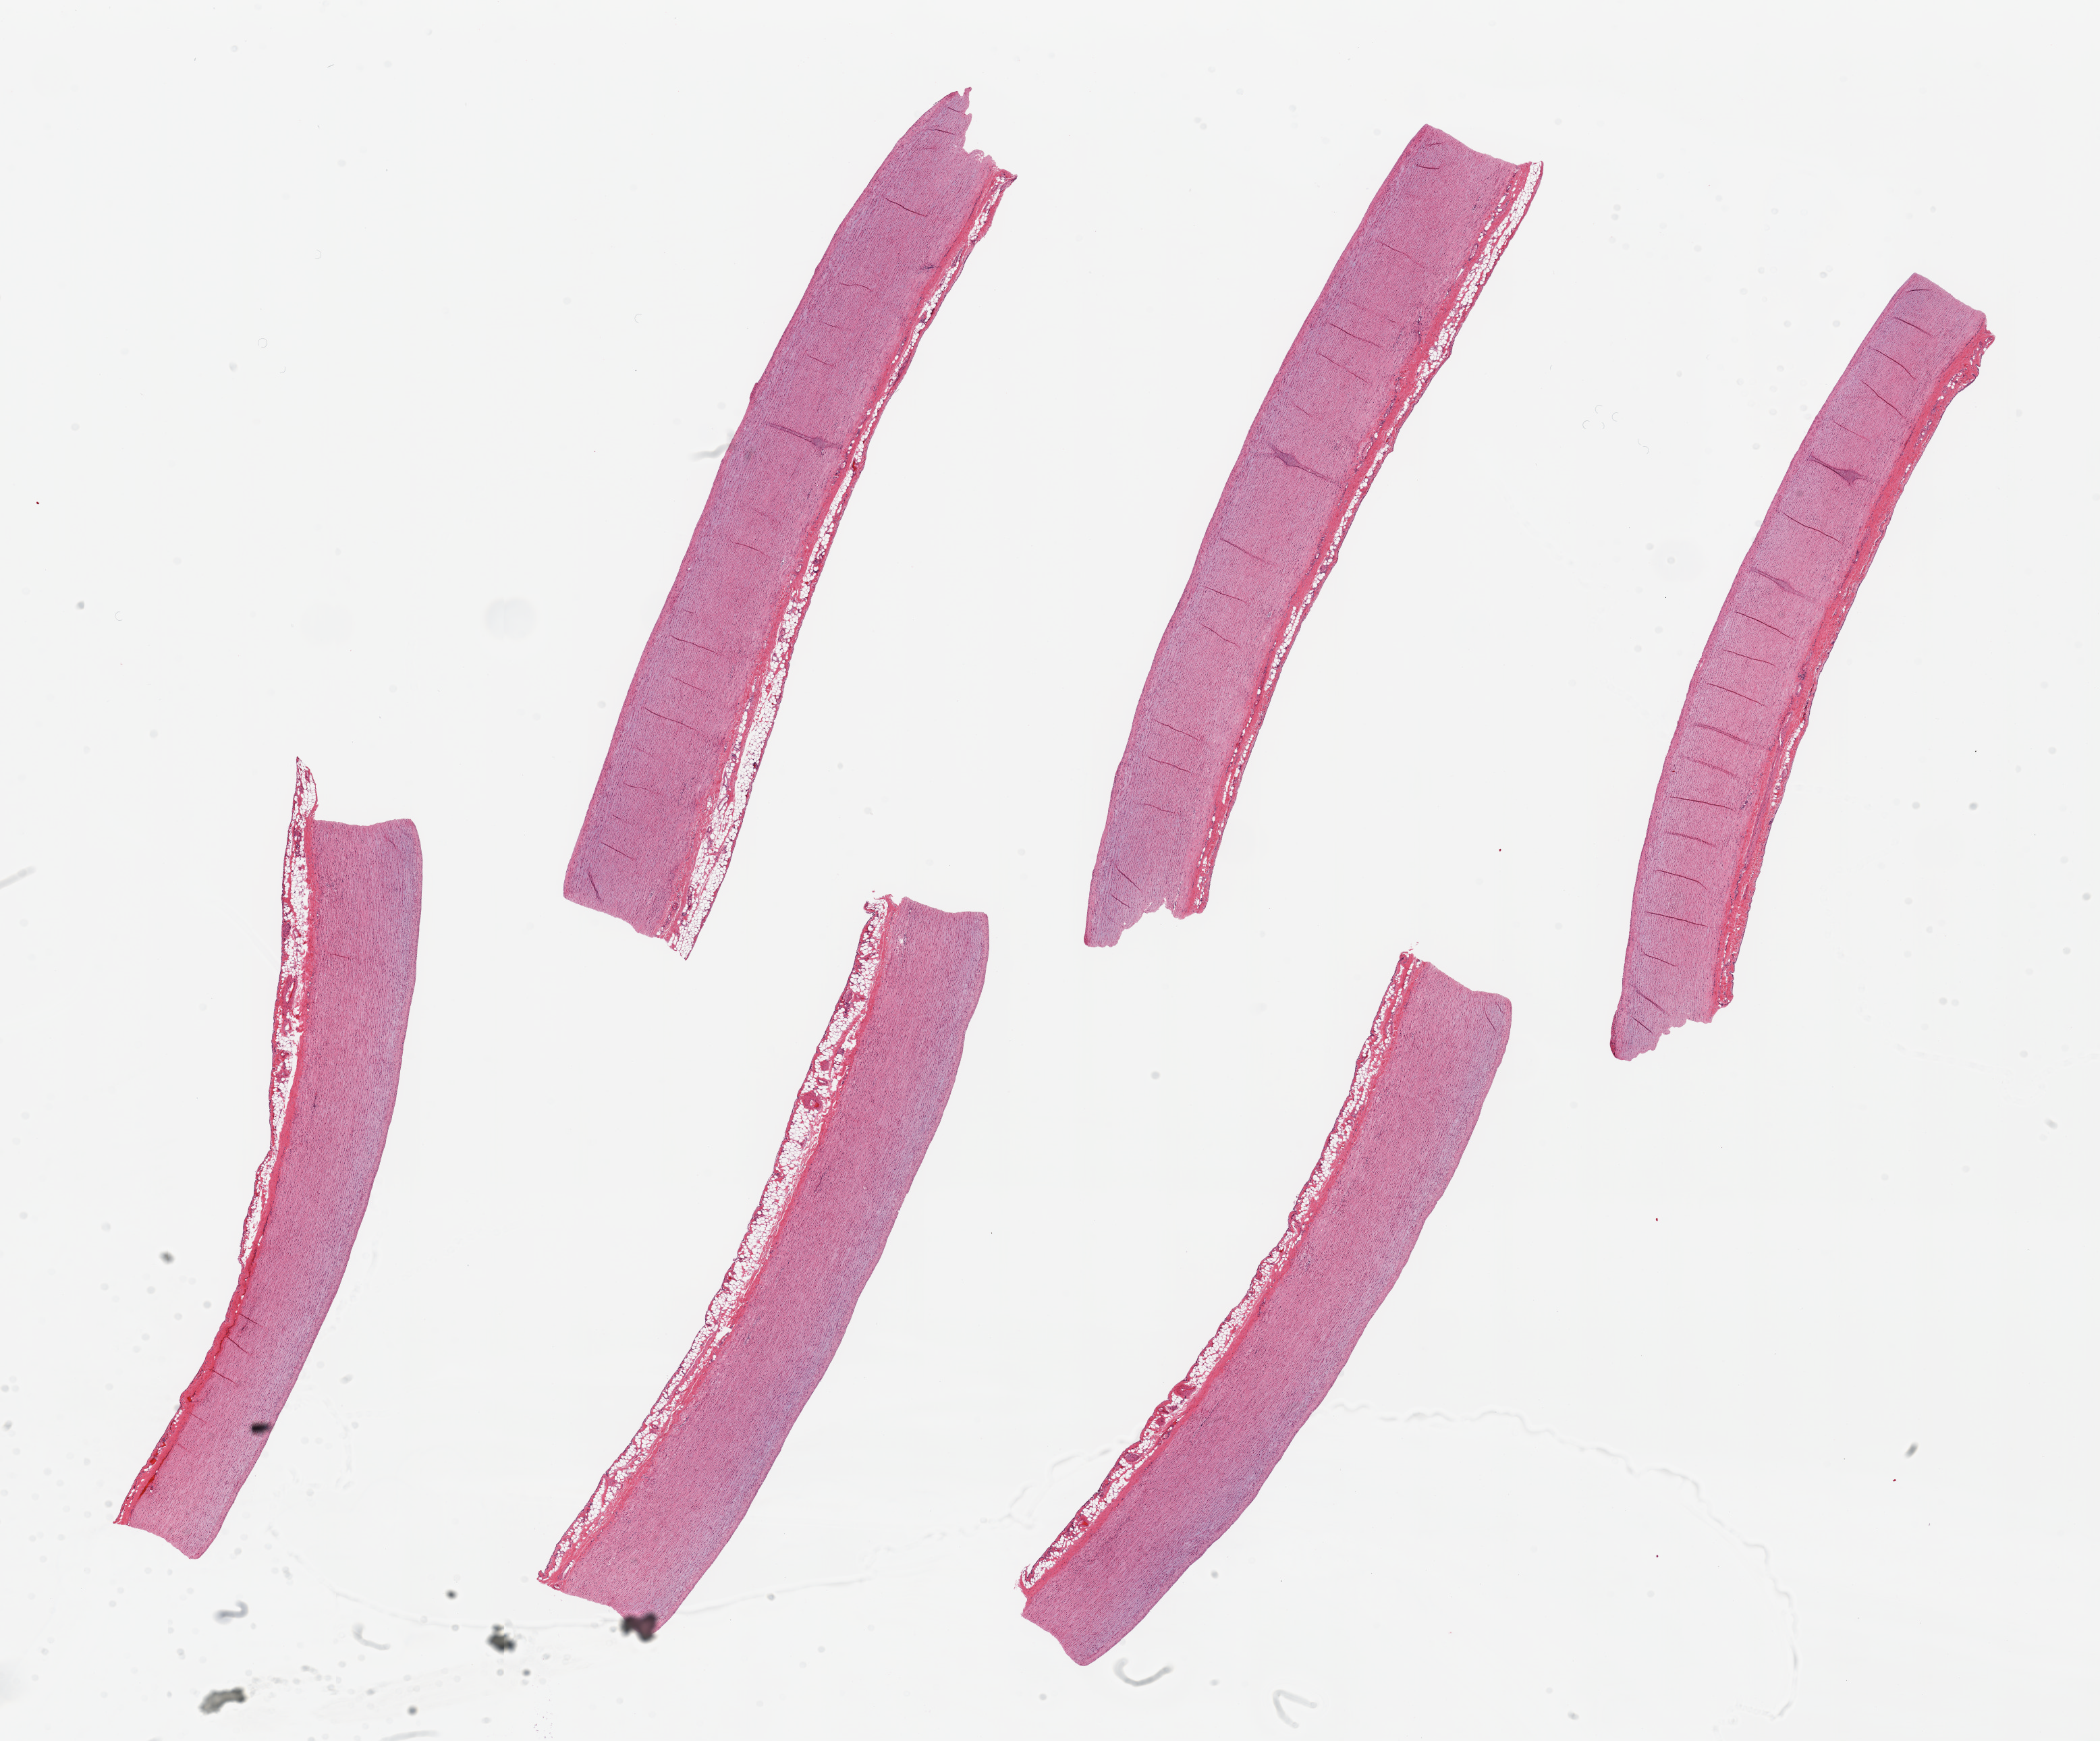
H&E whole-slide image, whole scanned area (about 24.6 x 20.4 mm) shown as a low-resolution overview; PAXgene-fixed, paraffin-embedded tissue; section of aorta (target tissue); donor tissue sample.
Pathologist's review note for this sample: 6 pieces up to 10x1.5 mm; no plaques; good architecture.